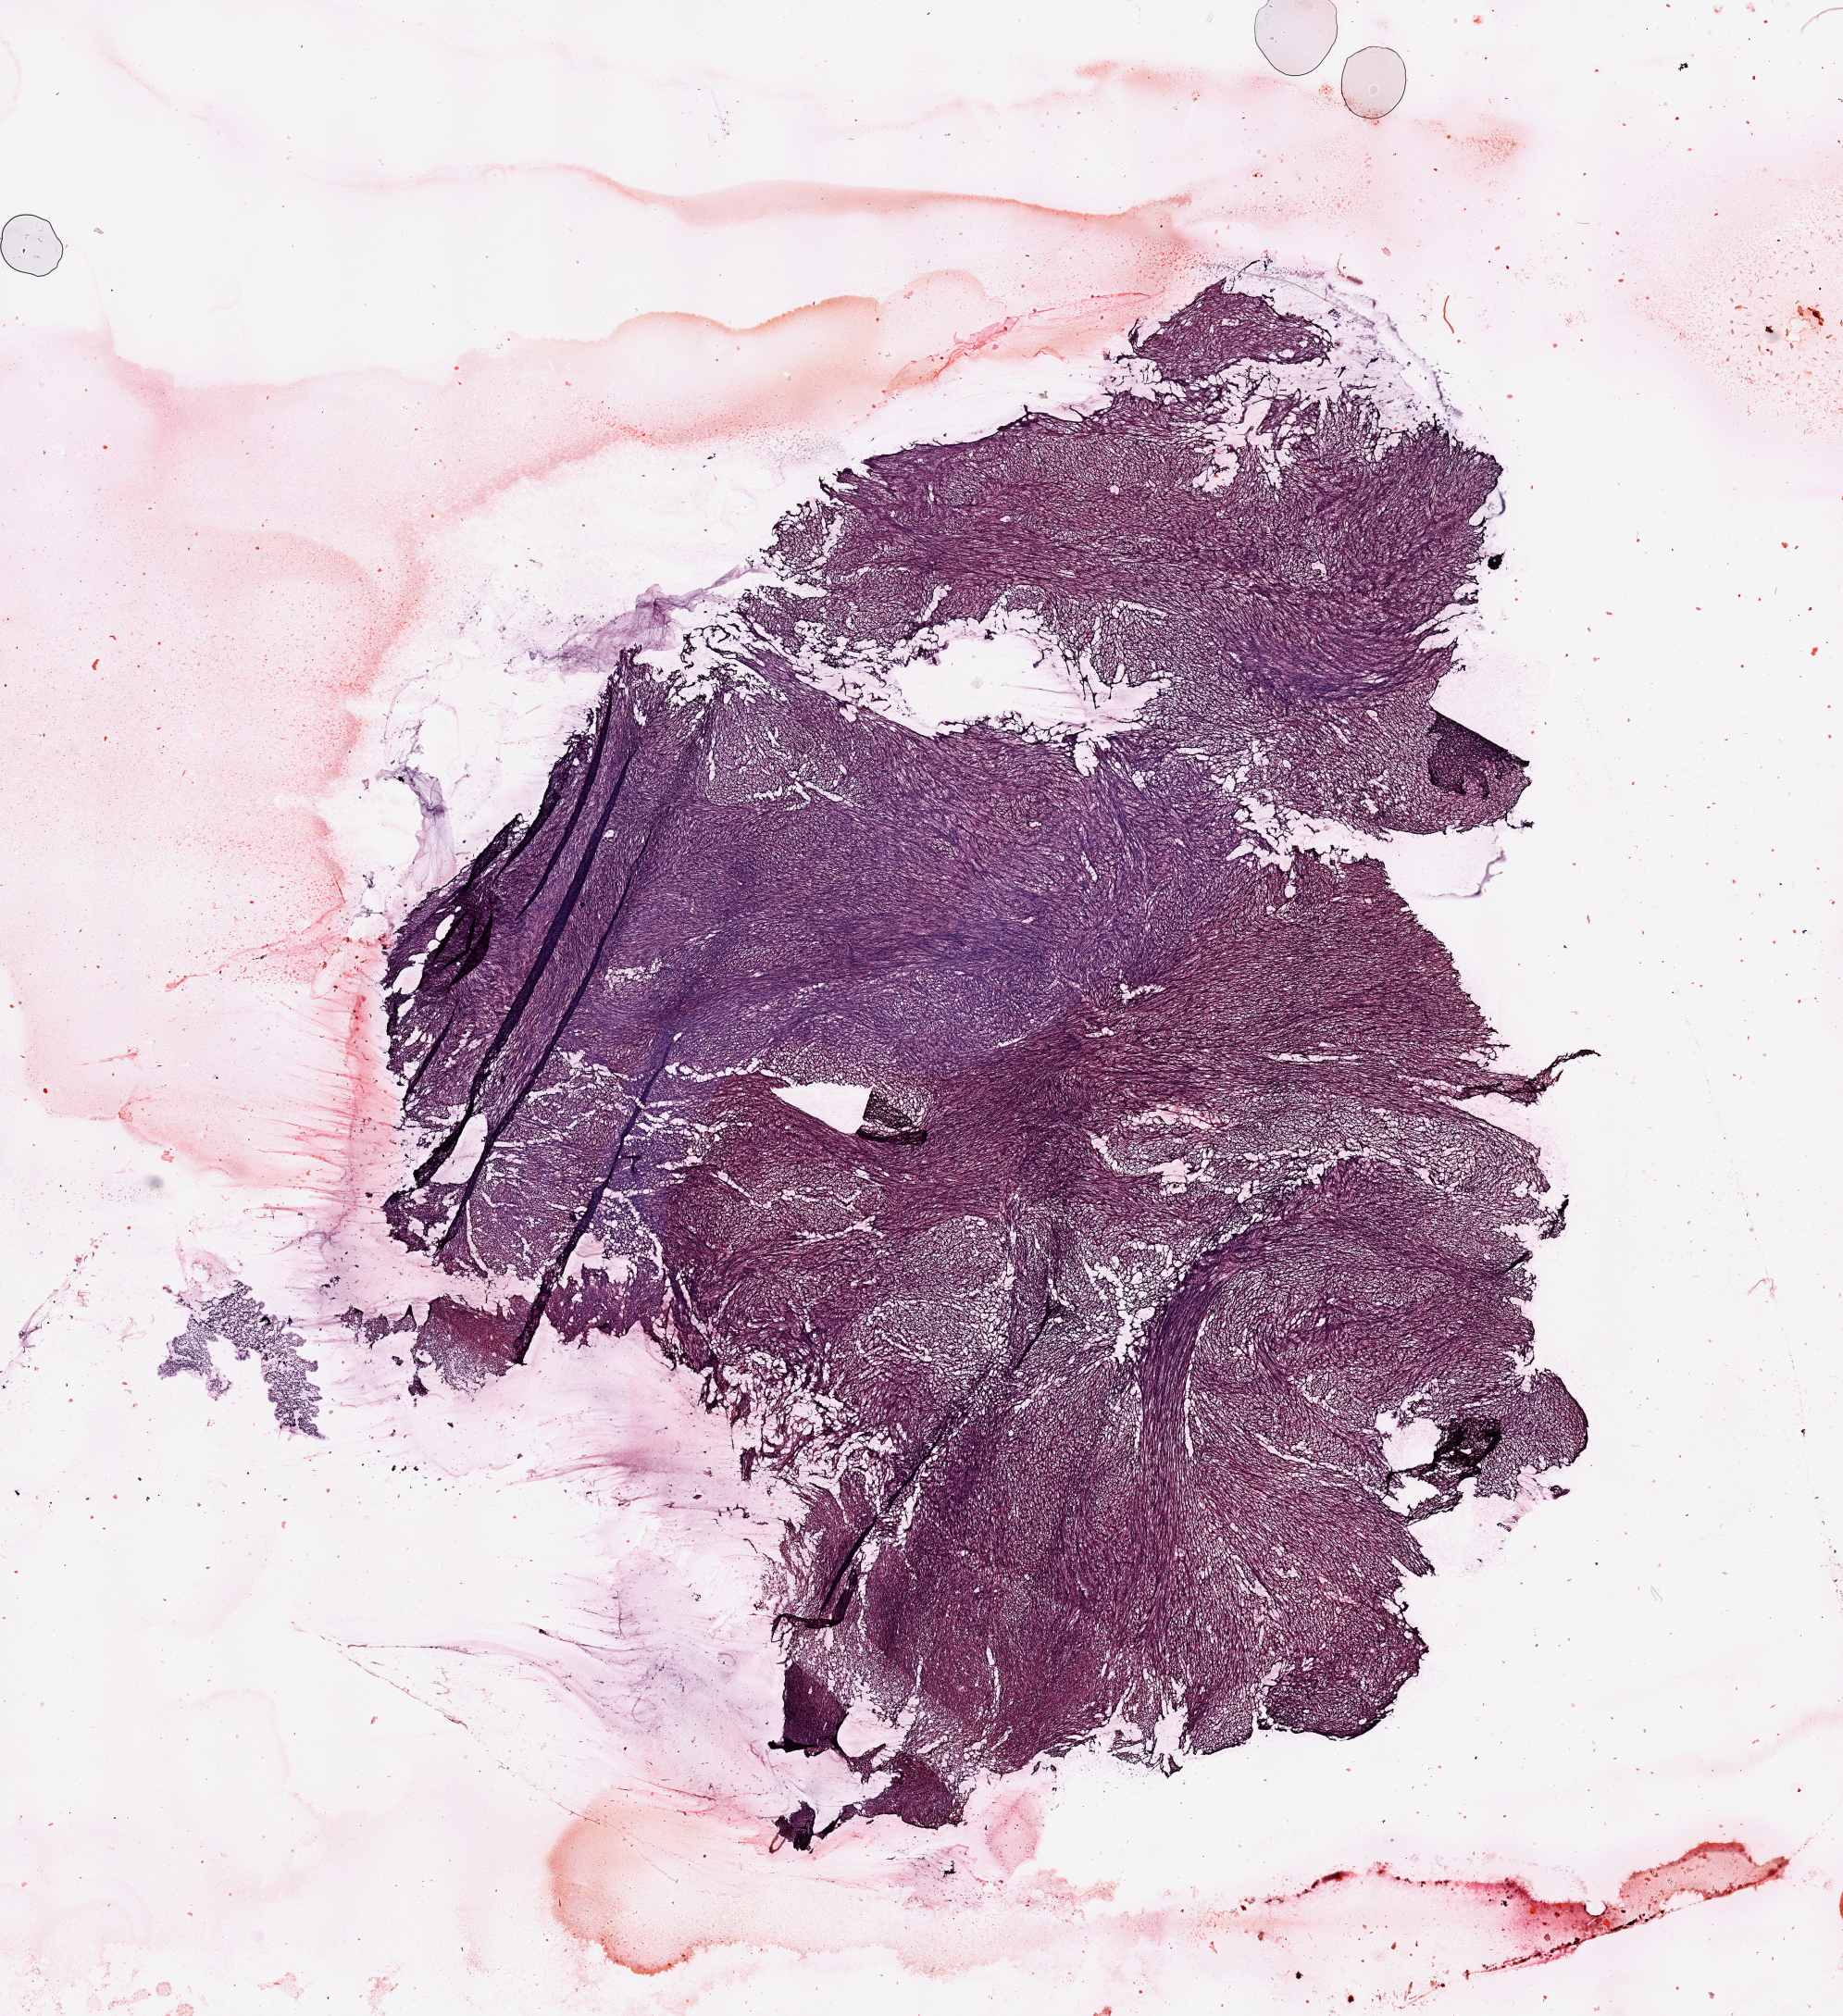
Digitized H&E-stained tissue section (whole slide) — a low-resolution overview of the entire scanned area, about 15.8 x 17.2 mm. Patient: female, age 65 years.
• patient diagnosis (cohort enrolment): sarcoma (site not recorded at cohort level)
• primary tumour site (as recorded): gynecologic